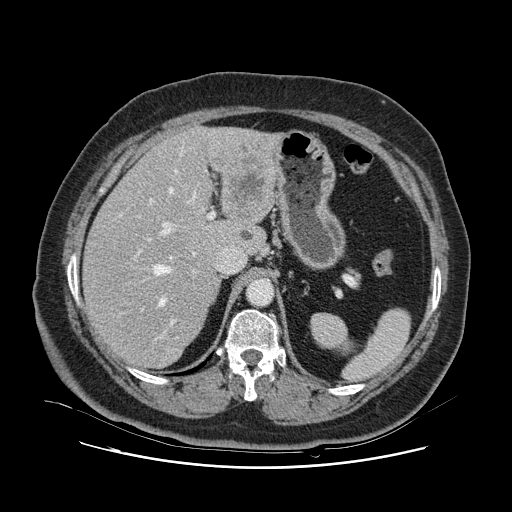
Contrast-enhanced abdominal CT, one axial slice. Position 75 of 132 along the scan axis. Intravenous contrast given. Soft-tissue window (W 400 / L 40 HU). 2.5 mm slice thickness. 512 × 512 image matrix, field of view 391 × 391 mm. Female patient, age 73 years. Case-level facts recorded for this patient, not image findings: diagnosis: colorectal cancer liver metastases, imaged before liver resection; multiple liver metastases: no; largest metastasis: 7 cm; disease in both lobes: no.
Structures marked on this image (expert manual segmentation):
- hepatic veins: box from (x=132, y=148) to (x=196, y=306) px
- liver: (x=84, y=128)–(x=274, y=368)
- planned liver remnant (the part of the liver to remain after resection): (x=84, y=158)–(x=240, y=368)
- portal vein (with intrahepatic branches): (x=136, y=199)–(x=215, y=337)
- liver metastasis: (x=242, y=232)–(x=253, y=241)
- liver metastasis: (x=219, y=150)–(x=267, y=216)